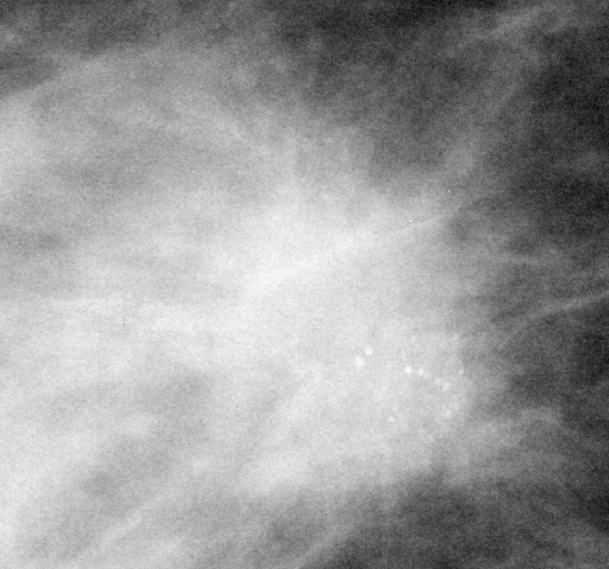
Region of interest cut from a scanned film mammogram (one marked finding); right breast; MLO view.
Finding: calcifications, morphology pleomorphic, distribution clustered / linear; BI-RADS assessment category 5; pathology result (as recorded, not read from the image): malignant.